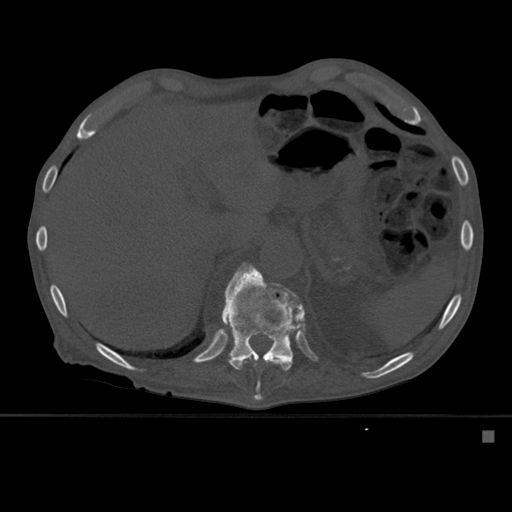
CT including the spine, one axial slice. Bone window (W 1800 / L 400 HU). 512 × 512 image matrix, field of view 373 × 373 mm. Male patient, age 78 years. Case-level facts recorded for this patient, not image findings: primary cancer: prostate.
Outlined on this slice (semi-automatic segmentation, software-assisted and operator-edited):
- T11 vertebra: box from (x=222, y=263) to (x=293, y=401) px
- T12 vertebra: (x=222, y=272)–(x=305, y=360)